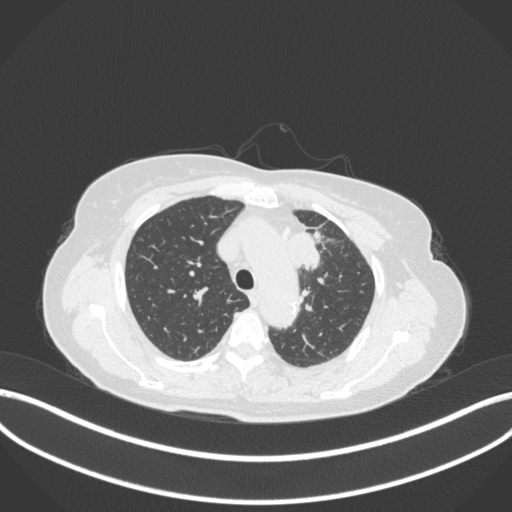
Chest CT, one axial slice. Slice 249 of 368 in the series (ordered by position). 120 kVp. Lung window (W 1500 / L -600 HU). 1 mm slice thickness. 512 × 512 image matrix, field of view 400 × 400 mm. Female patient, age 65 years. Case-level facts recorded for this patient, not image findings: clinical TNM (as recorded): T2a N0 M0; histopathological grade: G2-3.
Annotated regions visible in this slice (bounding box drawn by a radiologist):
- lung tumour (recorded histology: adenocarcinoma): bounding box <282,227,323,271> (left, top, right, bottom; pixels)